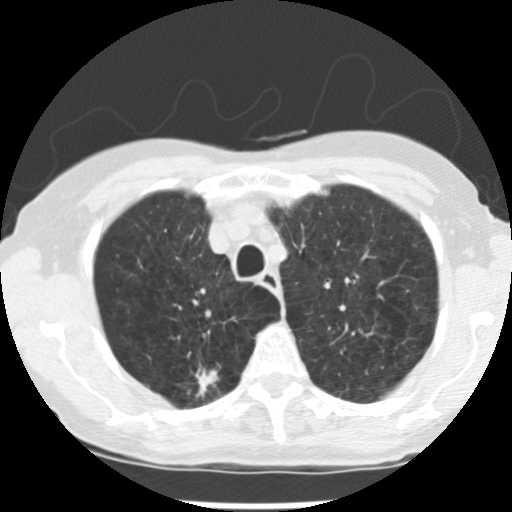
Chest CT (low-dose screening protocol), one axial image, baseline screening round, lung window (W 1500 / L -600 HU), 120 kVp. Female, age 72 years at enrolment. Current smoker at enrolment.
- Lesion marked by an expert reader, bounding box (x1, y1, x2, y2) in pixels: (183, 361, 234, 406).
- The screening reader recorded 3 non-calcified nodules or masses ≥4 mm on this exam (right upper lobe, left upper lobe, left lower lobe); which of them this box marks is not recorded.
- Lung cancer was diagnosed 50 days after this screen: adenocarcinoma, NOS, right upper lobe, moderately differentiated (G2), stage IB (AJCC 6th edition), 22 mm at pathology.